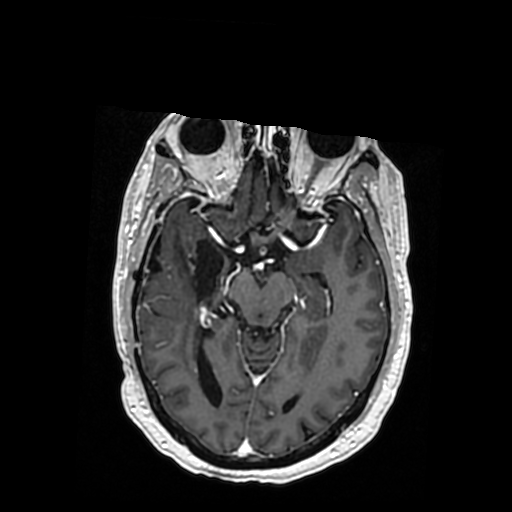
Brain MRI from a brain-tumour surgery series, one axial slice. T1-weighted post-contrast. 0.5 mm slice thickness. 512 × 512 image matrix, field of view 260 × 260 mm. From the clinical record (not read from this slice): histopathology: Oligodendroglioma; WHO grade: 3.
Annotated regions visible in this slice (expert manual segmentation):
- previous resection cavity: bounding box [x1, y1, x2, y2] px = [149, 238, 237, 300]